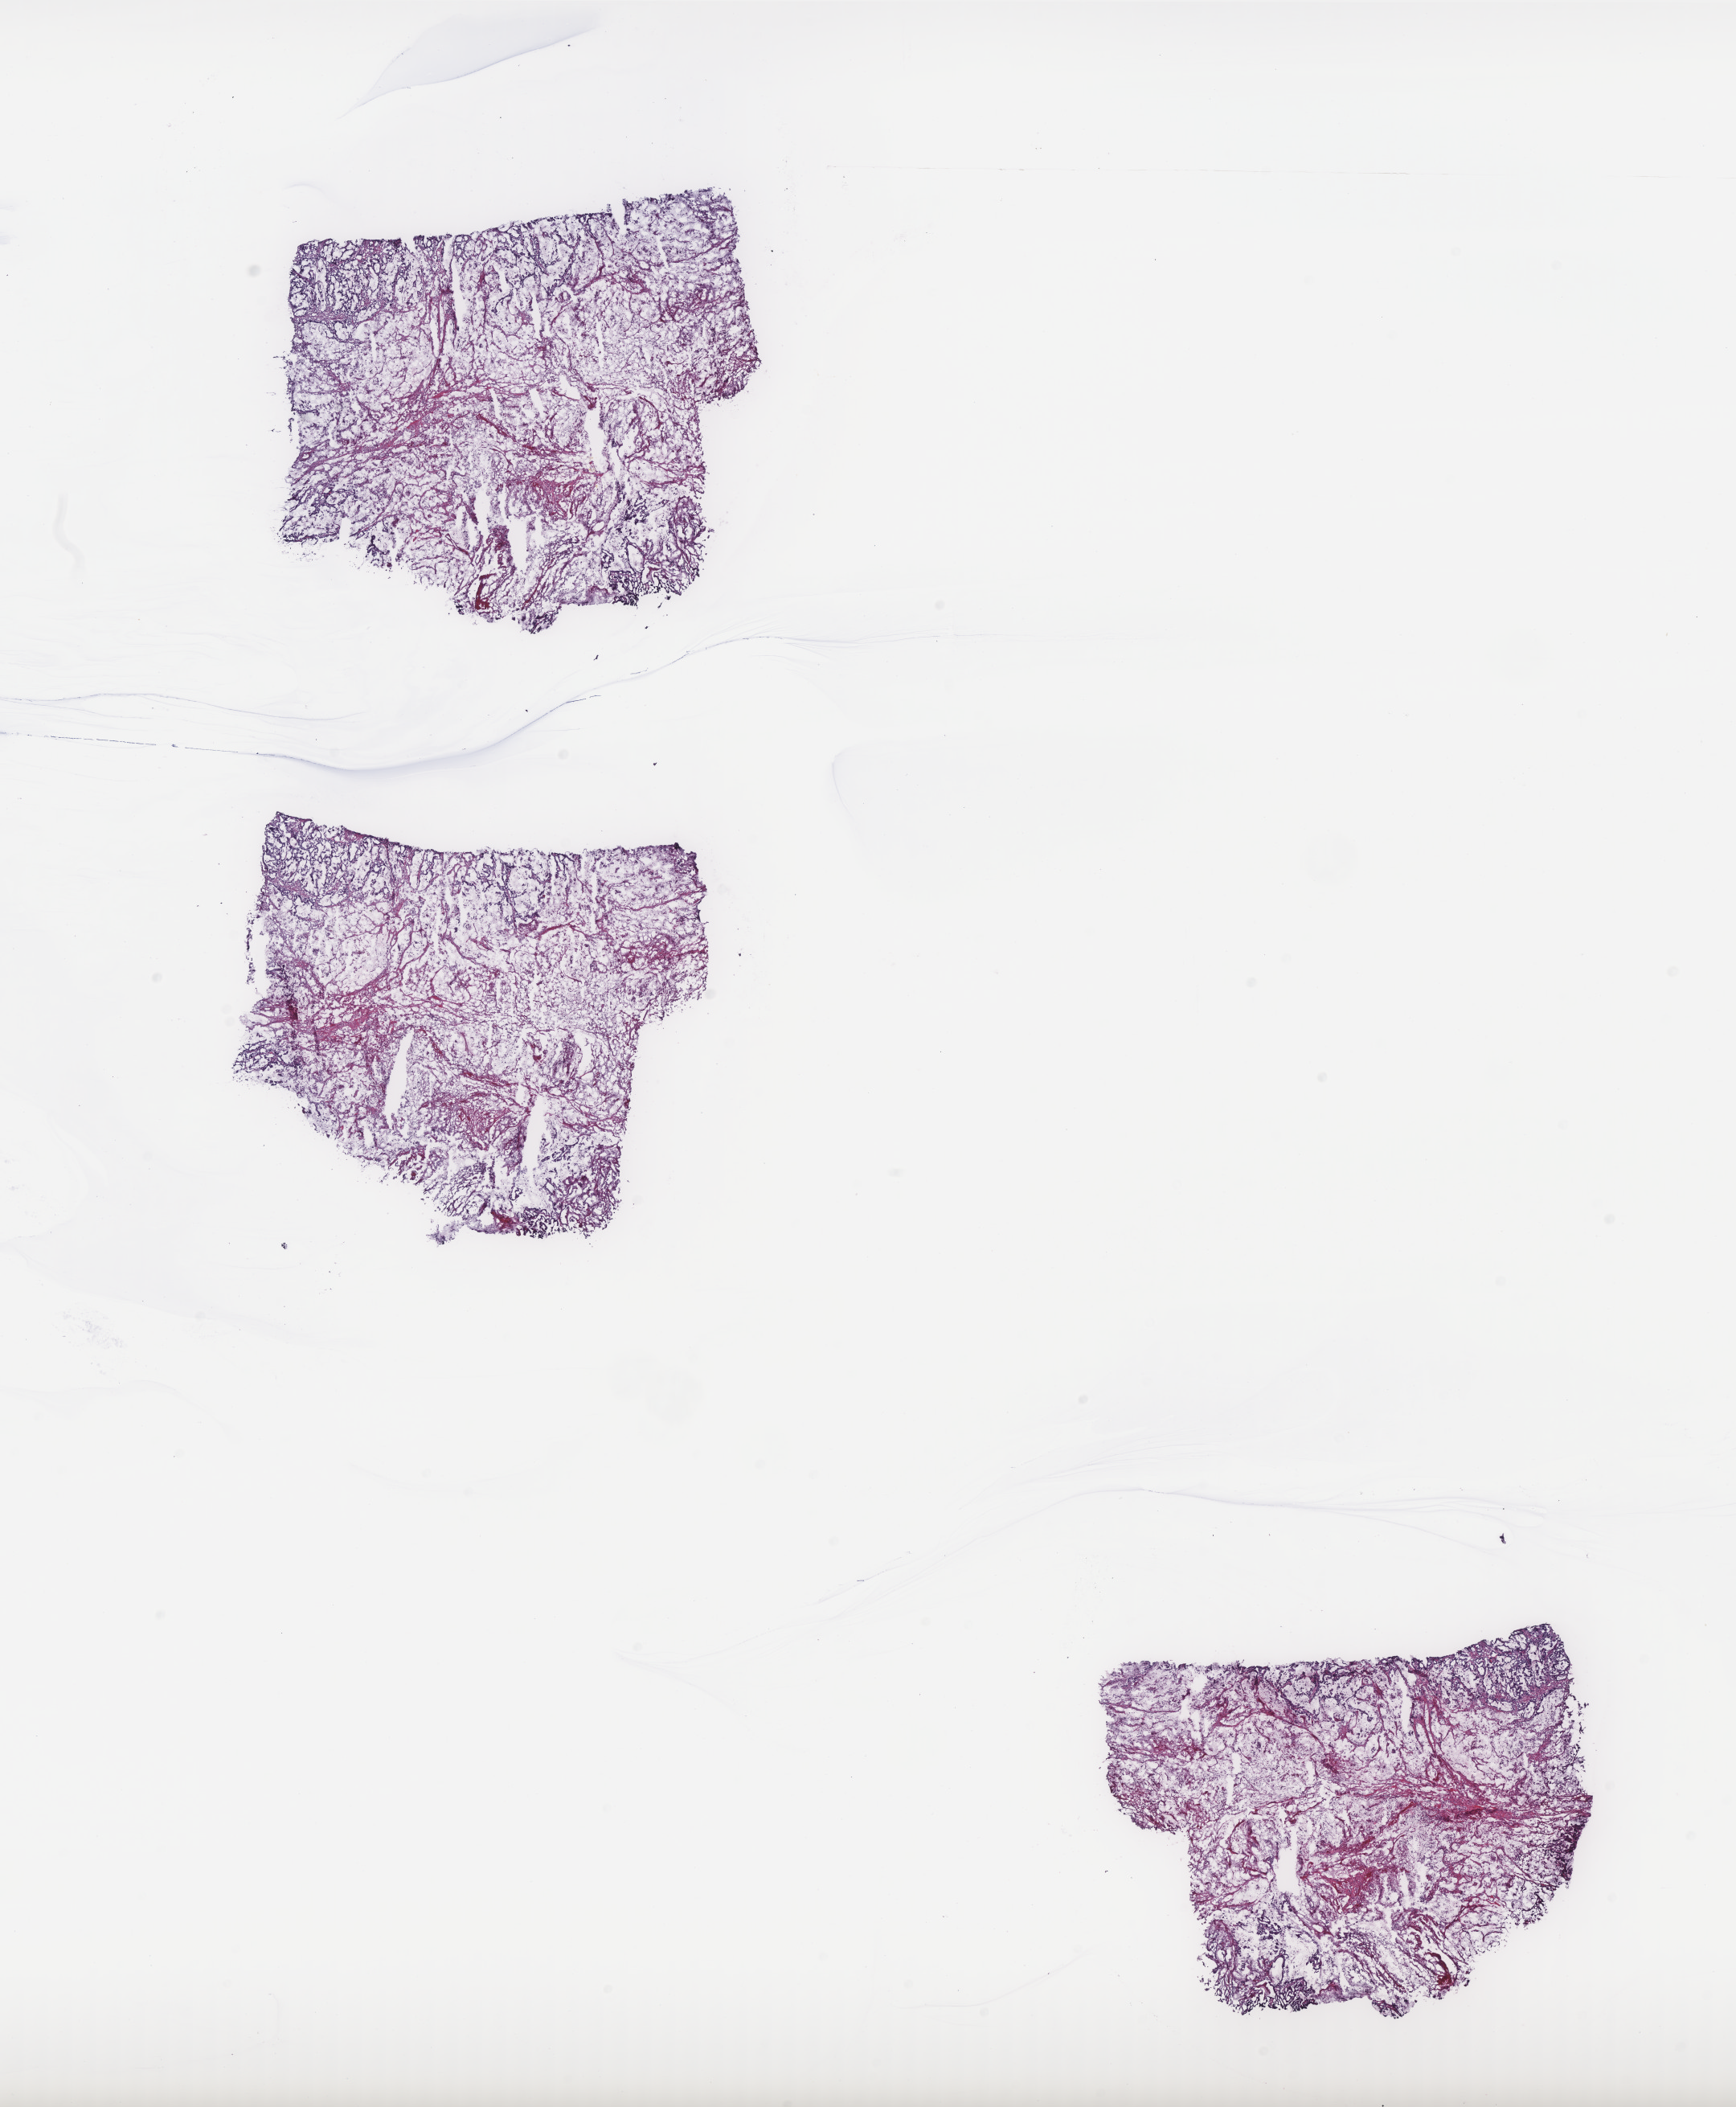
Digitized Hematoxylin and eosin (H&E) stained tissue section (whole slide) — whole scanned area (about 17.3 x 21.0 mm, from a 40x scan) shown as a low-resolution overview; frozen section from the top of the tissue portion; colon, primary tumour sample. Patient: male, age at initial diagnosis 75 years. Slide review estimates, as recorded: tumour cells 100%, tumour nuclei 70%, normal cells 0%, stromal cells 0%, necrosis 0%. Infiltration values recorded for this section: lymphocyte infiltration 0%, monocyte infiltration 0%, neutrophil infiltration 0%.
AJCC pathologic stage: IIIB. Histologic diagnosis: Mucinous adenocarcinoma (transverse colon).